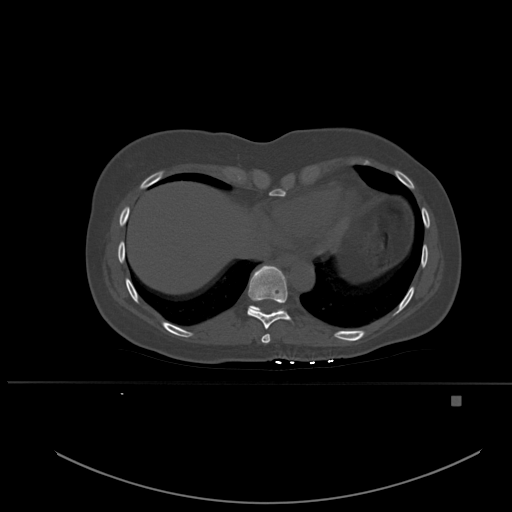
CT including the spine, one axial slice; slice 303 of 651 in the series (ordered by position); bone window (W 1800 / L 400 HU); 1.5 mm slice thickness; 512 × 512 image matrix. Female patient, age 49 years. Case-level facts recorded for this patient, not image findings: primary cancer: breast; vertebrae with lytic lesions (as recorded): L3, T12, L4.
Structures marked on this image (semi-automatic segmentation, software-assisted and operator-edited):
- T10 vertebra: bounding box (x1, y1, x2, y2) in pixels: (250, 305, 284, 315)
- T8 vertebra: (261, 334, 270, 343)
- T9 vertebra: (247, 265, 291, 329)